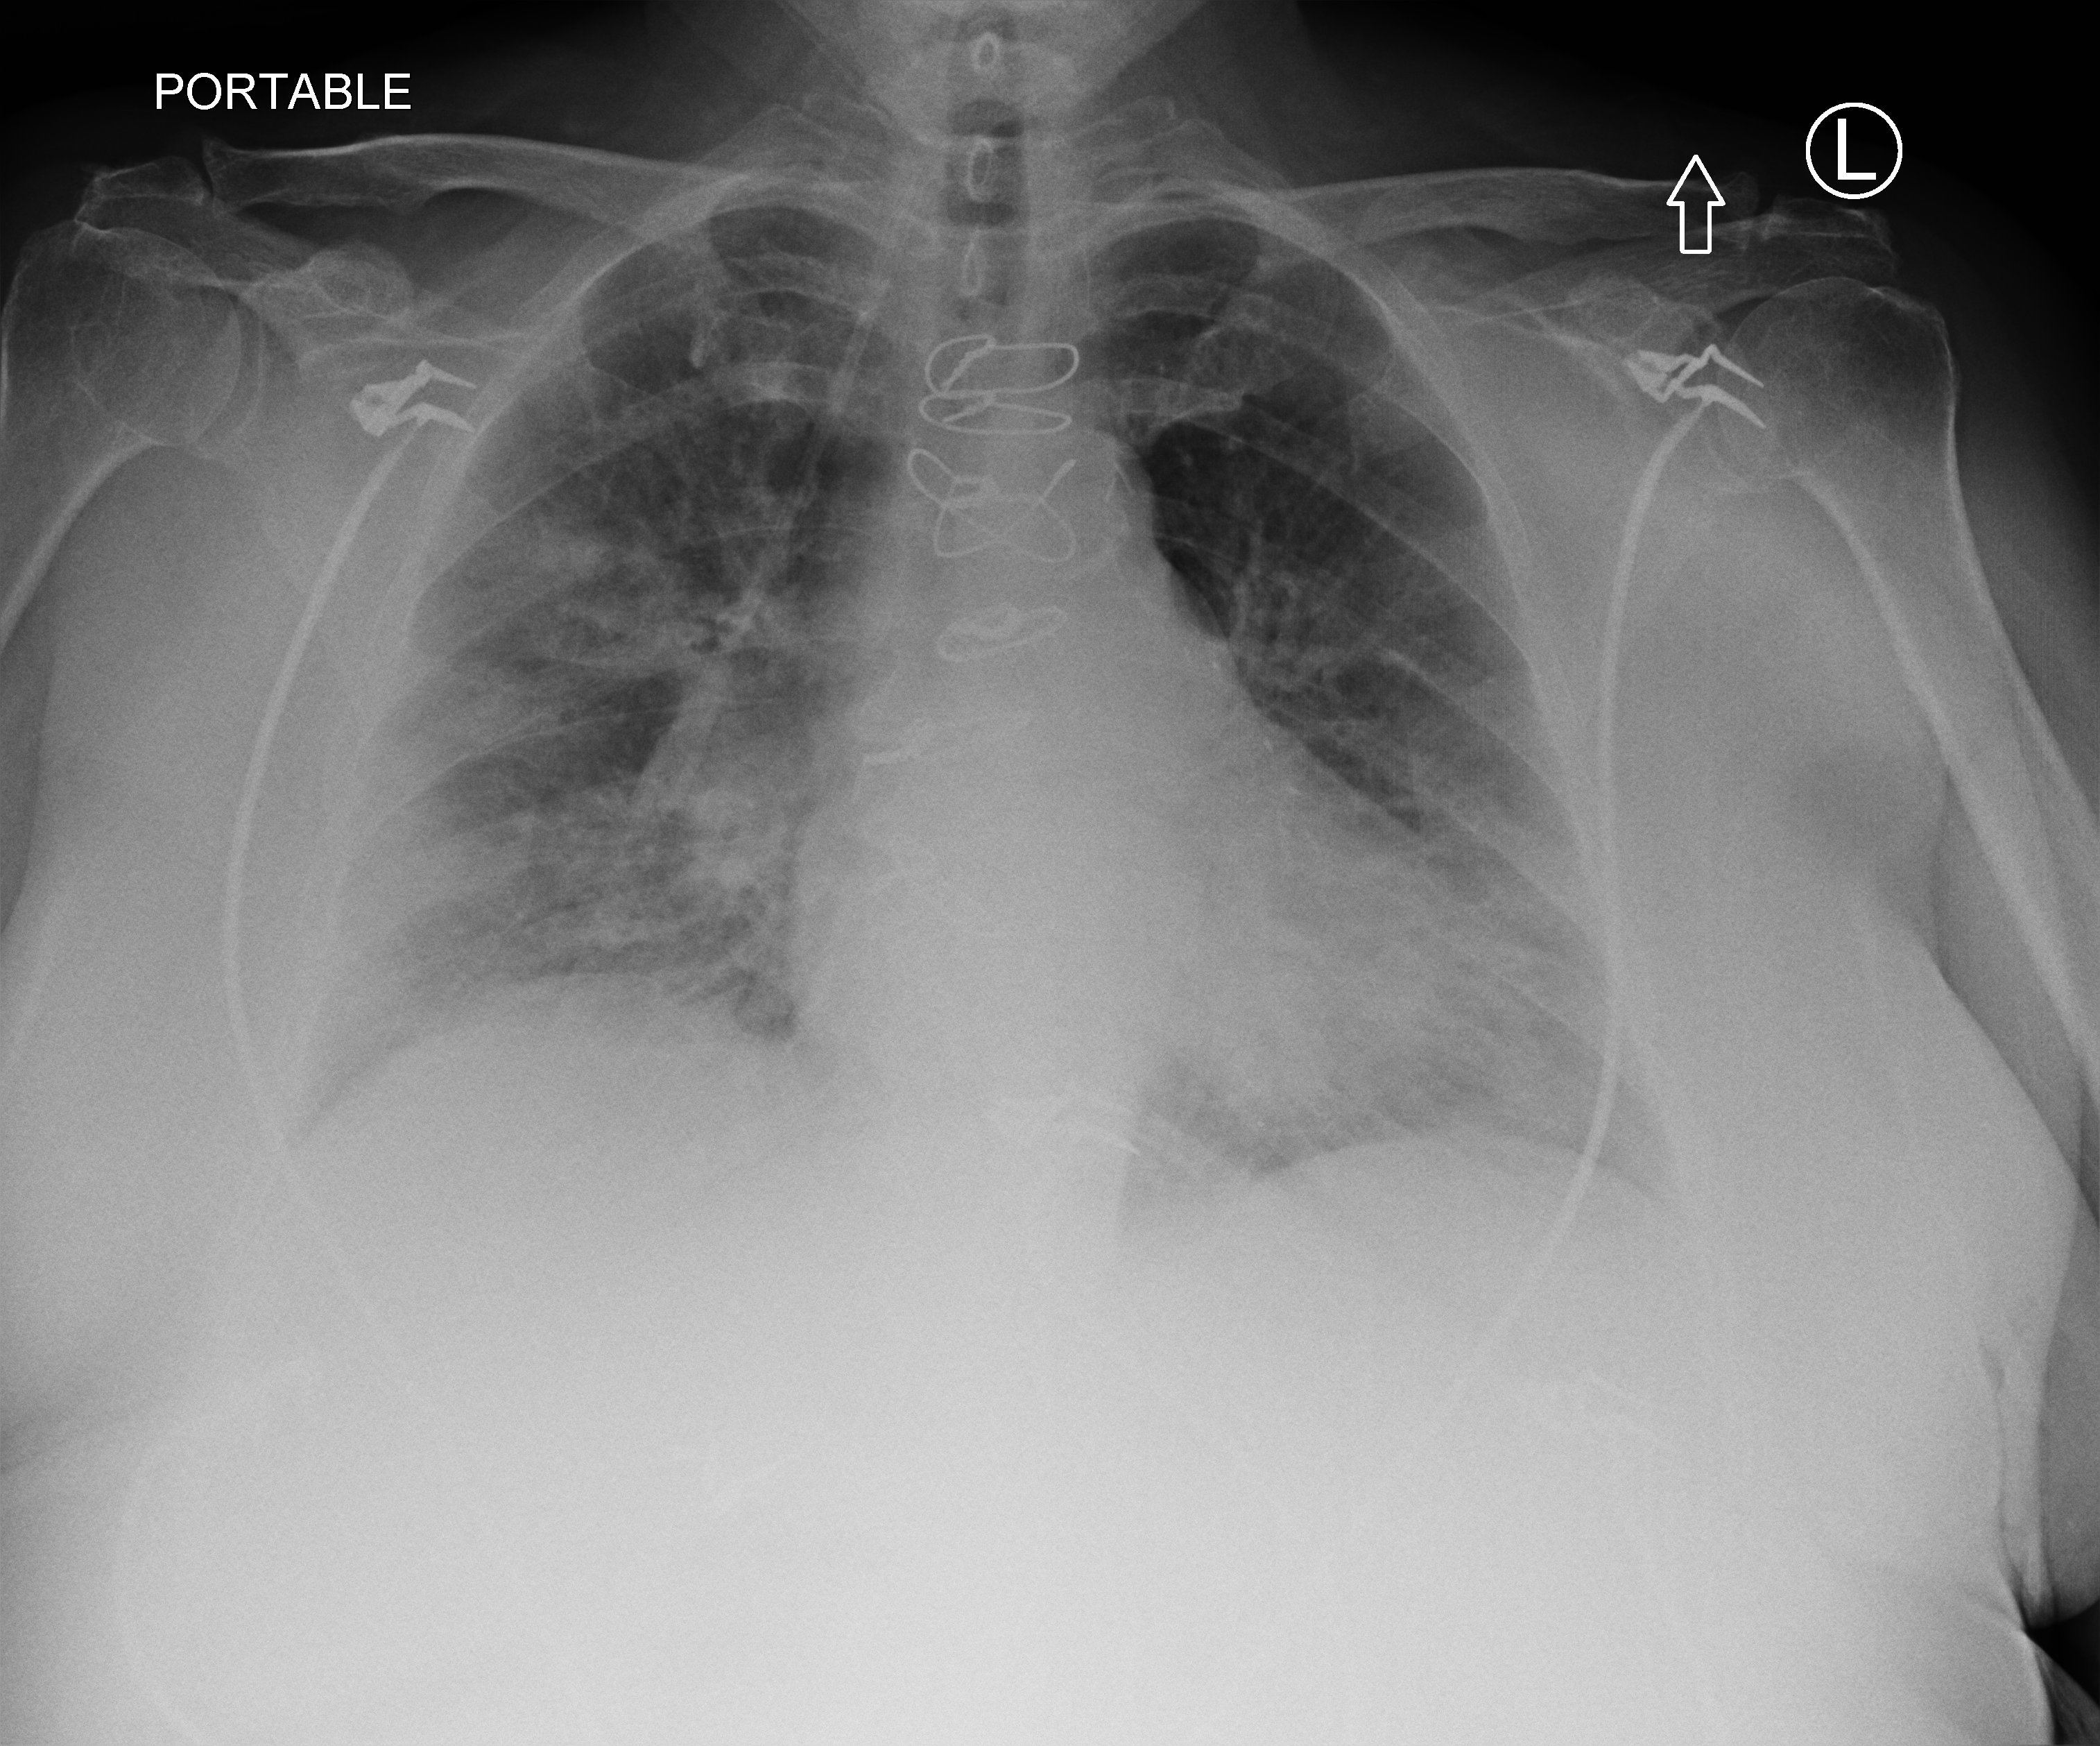
Chest X-ray (portable); anteroposterior (AP) projection. Female patient hospitalised with COVID-19, age 60–74 years.
Admission-level facts for this patient (not findings on this image; timing relative to this image not recorded): smoking status (admission record): former; admitted to intensive care during this hospital stay: no; mechanically ventilated during this hospital stay: no.